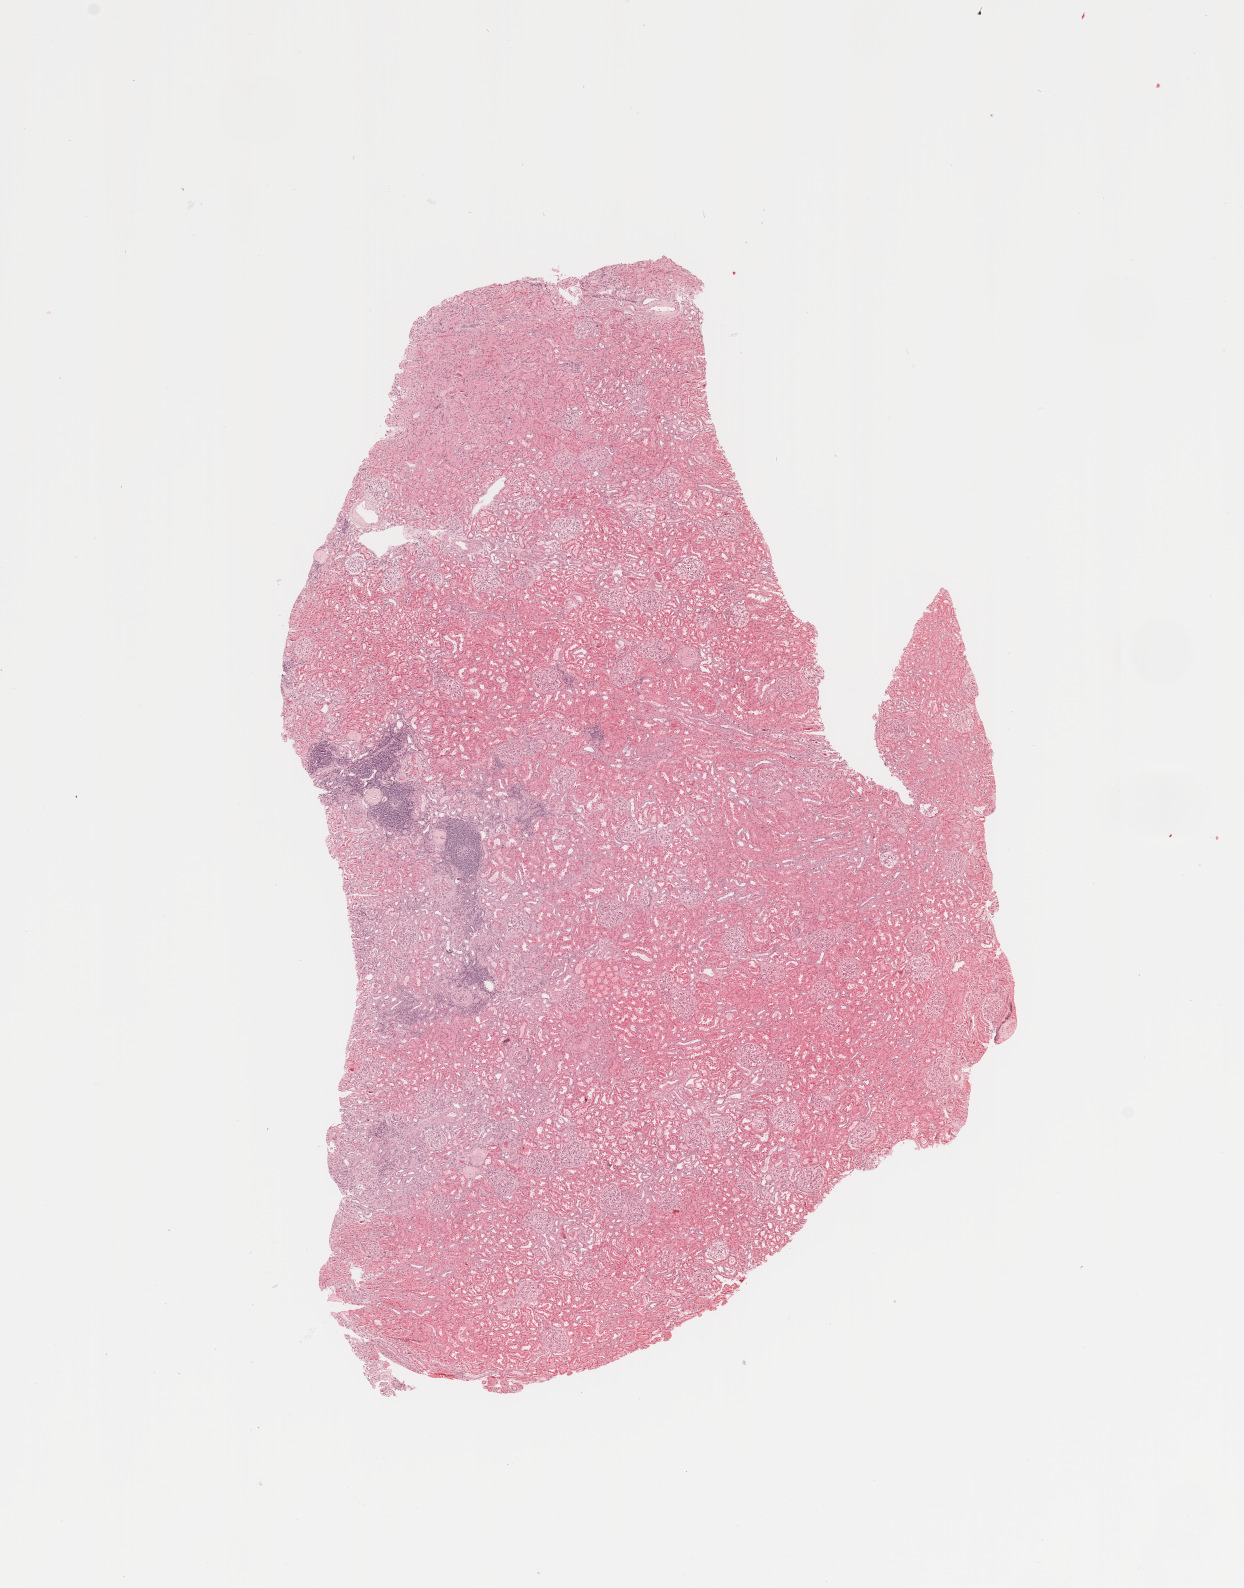
Whole-slide histology image, Hematoxylin and eosin (H&E) stained — low-resolution overview of the scanned area, about 9.8 x 12.6 mm (acquisition: 20x scan); kidney, normal (non-tumour) tissue. 66-year-old female patient.
• this section: normal (non-tumour) tissue from the same patient
• patient diagnosis: Renal cell carcinoma, NOS